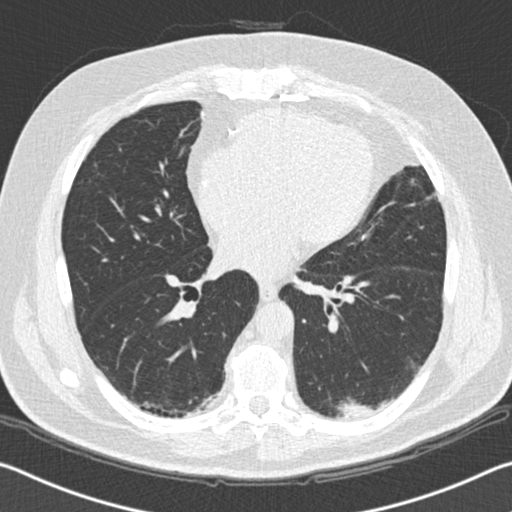
Low-dose screening chest CT, one axial slice. Position 82 of 172 along the scan axis. 120 kVp. Lung window (W 1500 / L -600 HU). 512 × 512 image matrix, field of view 340 × 340 mm.
Outlined on this slice (outlined manually by an expert reader):
- lesion 1 (tumor, lower lobe of left lung): box from (x=337, y=398) to (x=375, y=419) px